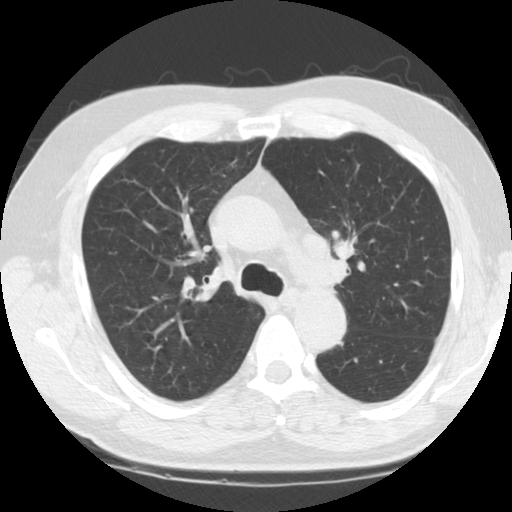
Low-dose screening chest CT, one axial slice. Position 86 of 124 along the scan axis. Reconstruction kernel STANDARD. 120 kVp. Lung window (W 1500 / L -600 HU). 2.5 mm slice thickness. 512 × 512 image matrix, field of view 340 × 340 mm.
Outlined on this slice (outlined manually by an expert reader):
- lesion 1 (tumor, upper lobe of left lung): box from (x=334, y=233) to (x=355, y=261) px